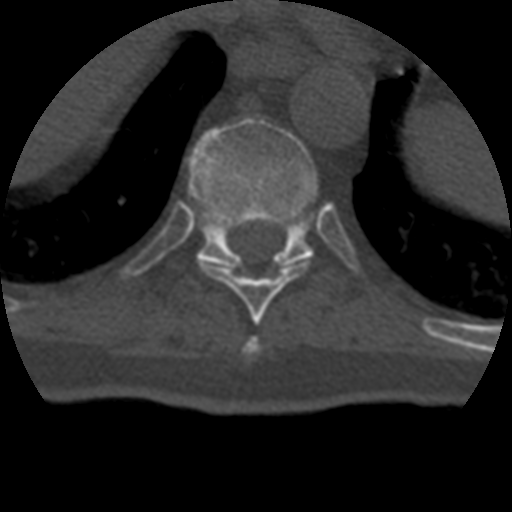
CT including the spine, one axial slice; slice 230 of 399 in the series (ordered by position); reconstruction kernel STANDARD; 120 kVp; bone window (W 1800 / L 400 HU); 1.25 mm slice thickness; 512 × 512 image matrix, field of view 160 × 160 mm. Patient age 69 years. From the clinical record (not read from this slice): primary cancer: prostate.
Annotated regions visible in this slice (semi-automatic segmentation, software-assisted and operator-edited):
- T10 vertebra: bounding box <190,118,317,267> (left, top, right, bottom; pixels)
- T8 vertebra: <245,337,260,354>
- T9 vertebra: <202,262,307,321>